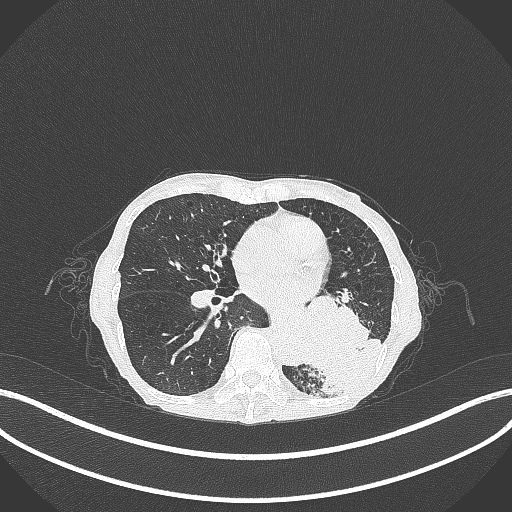
Chest CT, one axial slice. Slice 121 of 347 in the series (ordered by position). Reconstruction kernel B70f. Lung window (W 1500 / L -600 HU). 1 mm slice thickness. 512 × 512 image matrix, field of view 400 × 400 mm. Female patient, age 70 years. Case-level facts recorded for this patient, not image findings: clinical TNM (as recorded): T3 N0 M0; histopathological grade: G3.
Structures marked on this image (bounding box drawn by a radiologist):
- lung tumour (recorded histology: small cell carcinoma): bounding box (x1, y1, x2, y2) in pixels: (287, 291, 376, 383)